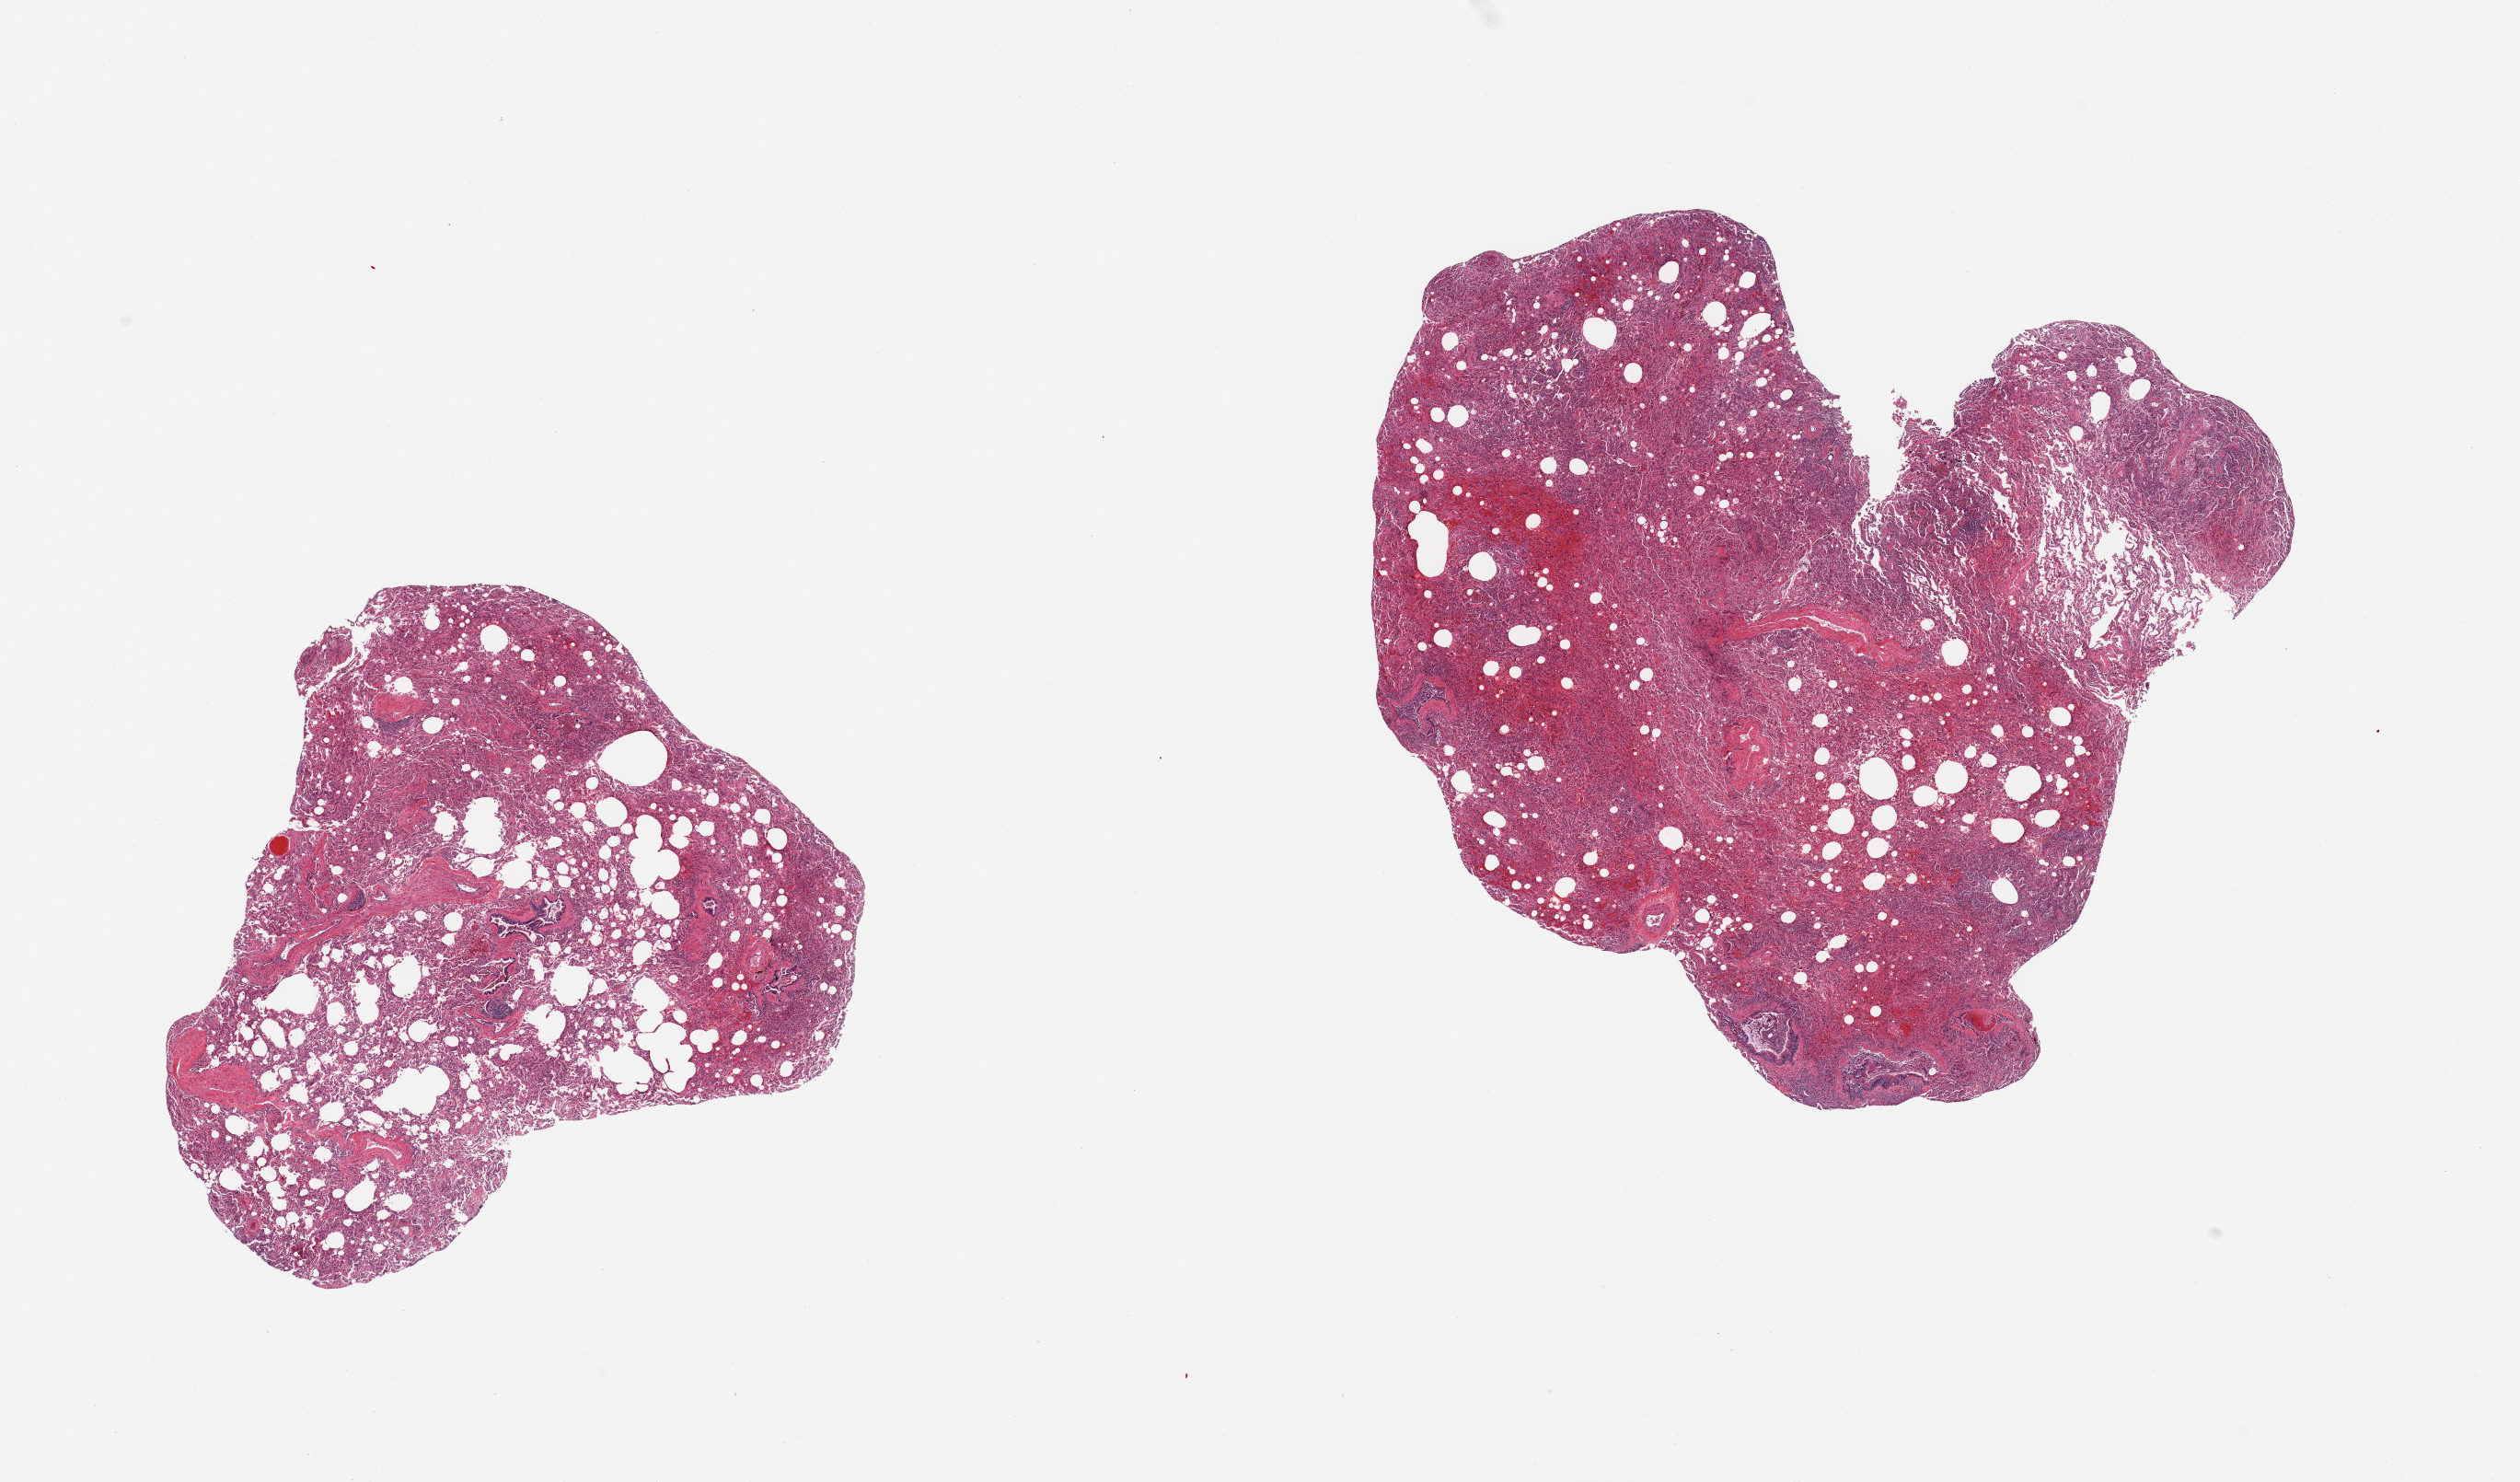
Whole-slide image, haematoxylin and eosin stain — shown as a low-resolution overview of the whole scanned area (about 21.7 x 12.7 mm), PAXgene-fixed paraffin-embedded (PFPE) section, sampled site (target tissue): lung, tissue donor sample. Donor: male.
- reviewer comment on this tissue sample: 2 pieces; some collapse, bronchopneumonia